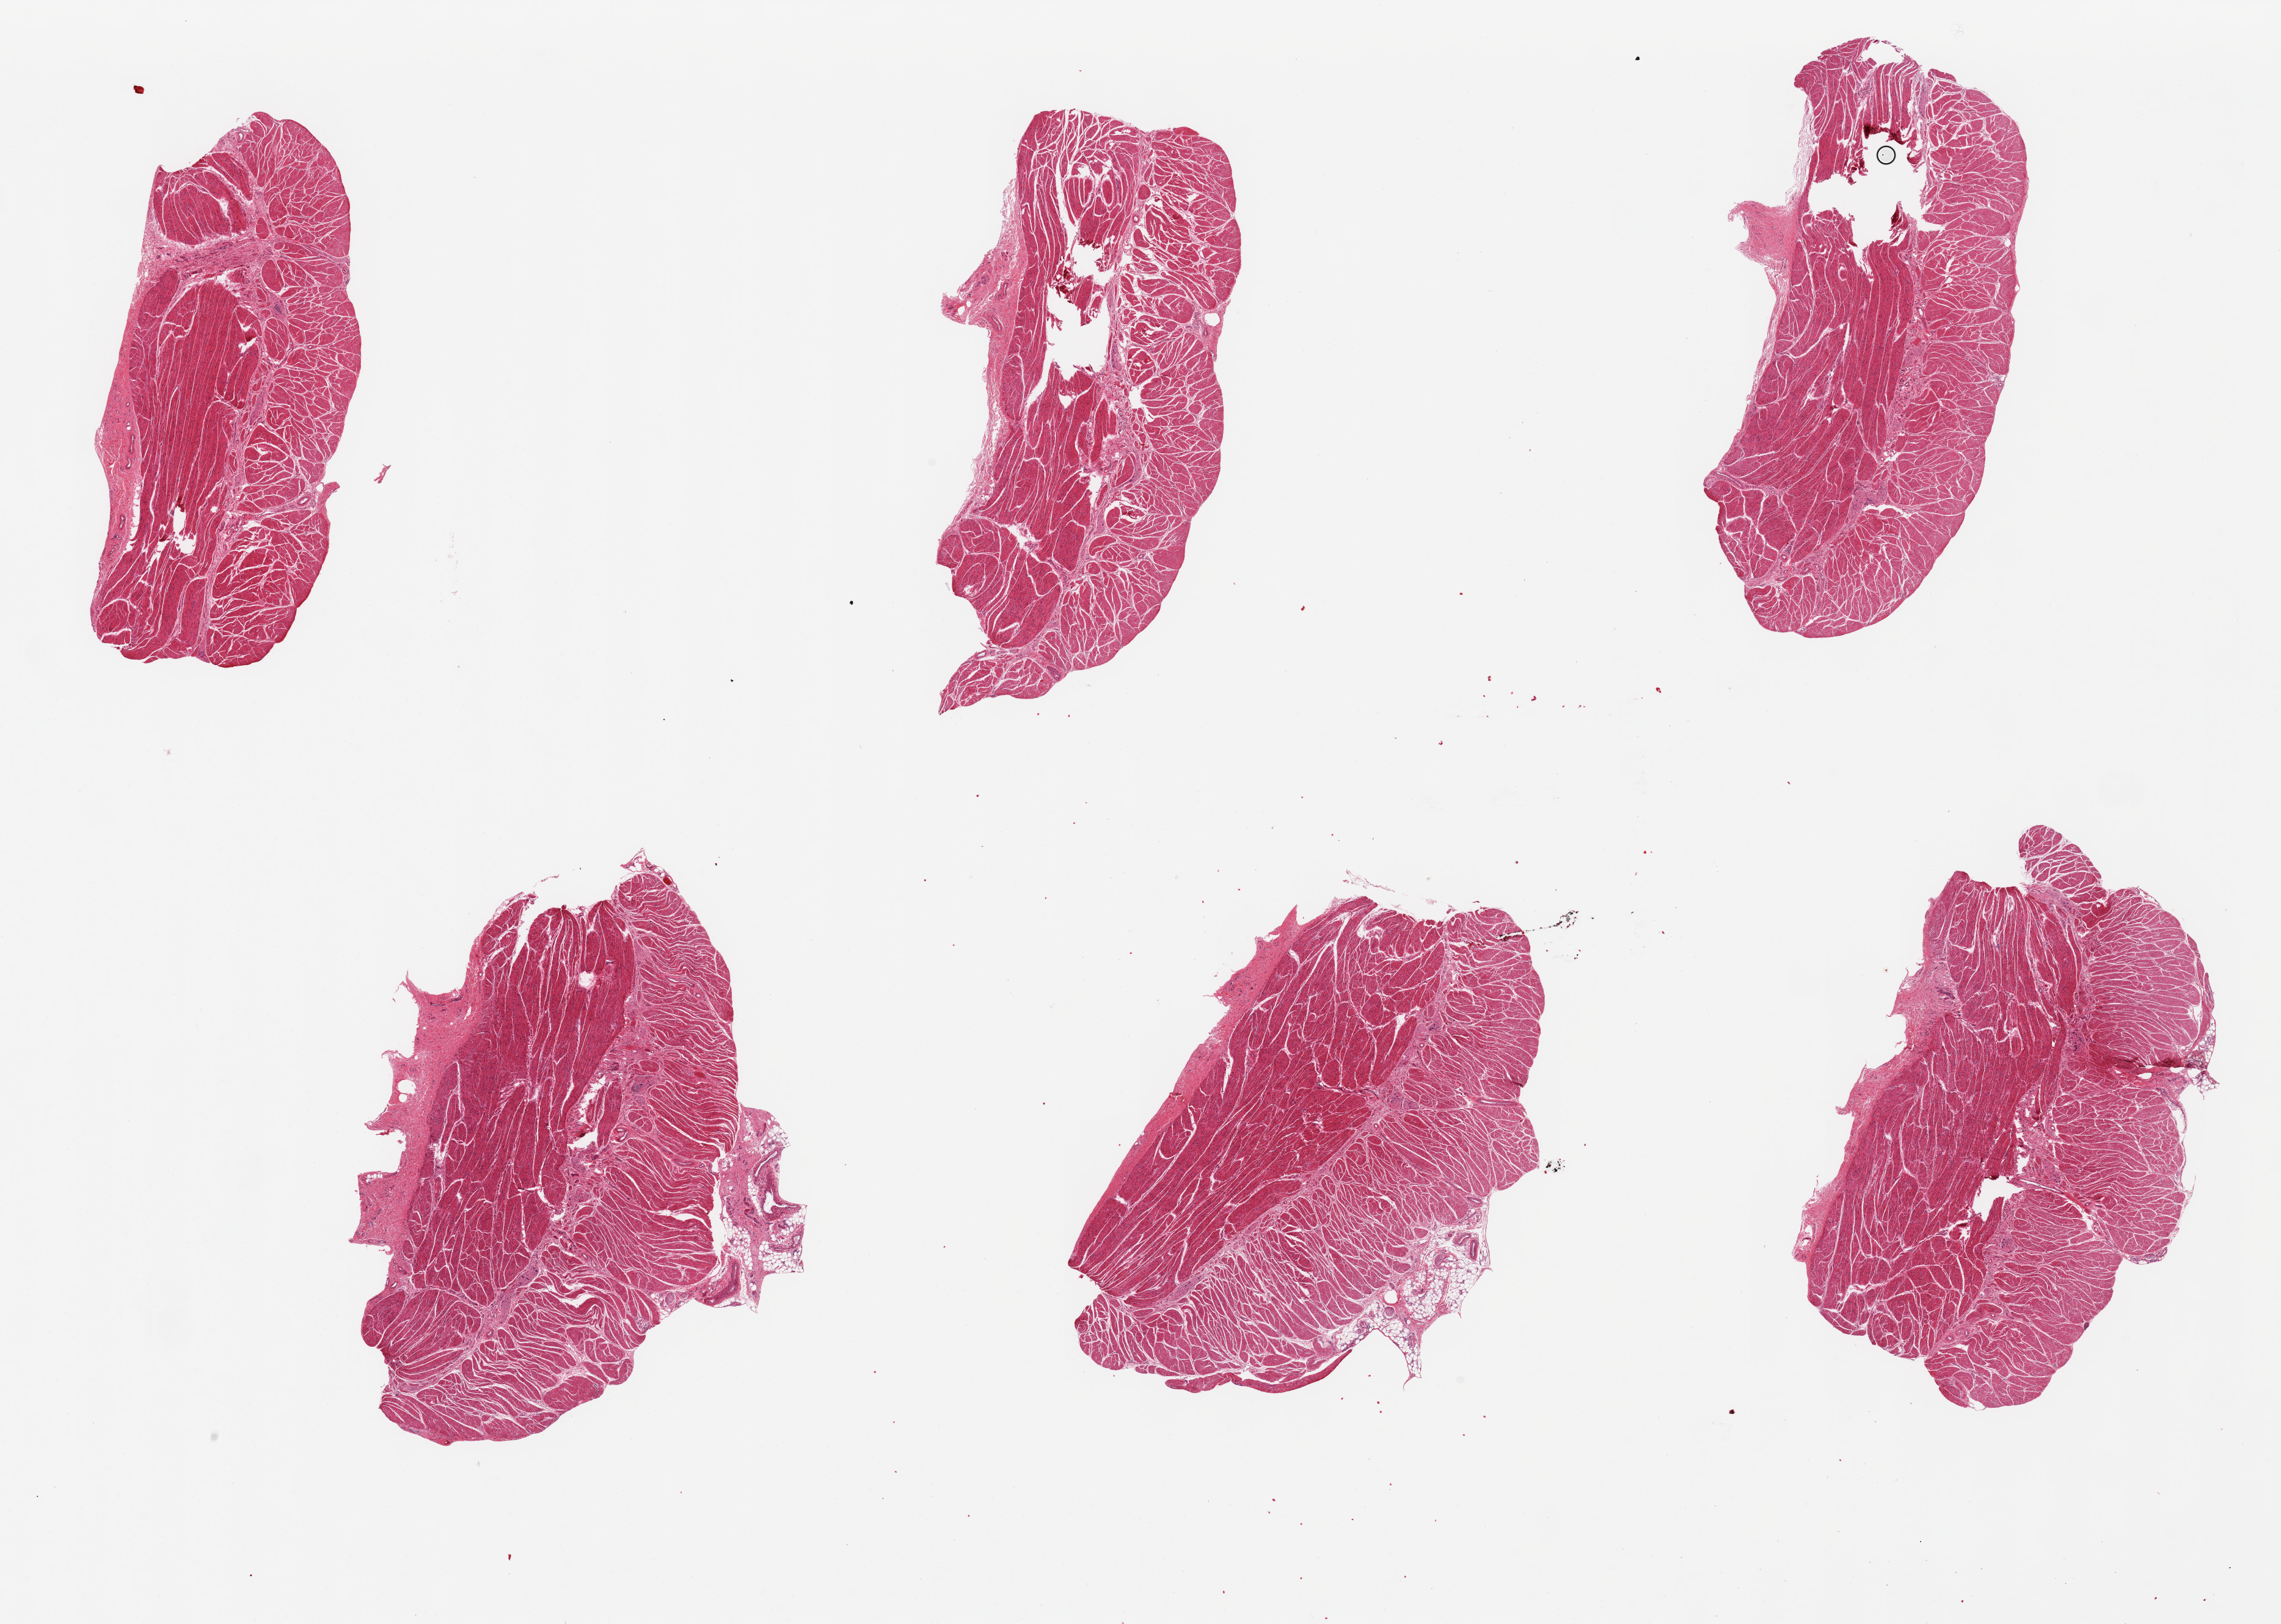
Digitized haematoxylin and eosin-stained section, brightfield — whole scanned area (about 29.5 x 21.0 mm) shown as a low-resolution overview; PAXgene-fixed paraffin-embedded (PFPE) section; target tissue: esophageal muscle; tissue donor sample.
Reviewer comment on this tissue sample: 6 pieces, up to 8x4mm; good specimen, minimal adipose.